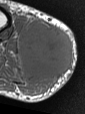
MRI of an extremity soft-tissue mass, one axial slice; slice 20 of 47 in the series (ordered by position); MR volume resampled by the dataset authors to the PET/CT grid (not the native acquisition matrix); 3.27 mm slice thickness; 85 × 114 image matrix. Male patient. From the clinical record (not read from this slice): histological type: pleiomorphic liposarcoma; grade: high; site of the primary tumour: right calf.
Annotated regions visible in this slice (expert contour drawn on MRI and transferred to this co-registered scan by the dataset authors):
- gross tumour volume including surrounding oedema: bounding box [x1, y1, x2, y2] px = [19, 18, 75, 95]
- gross tumour volume (mass): [20, 23, 75, 79]